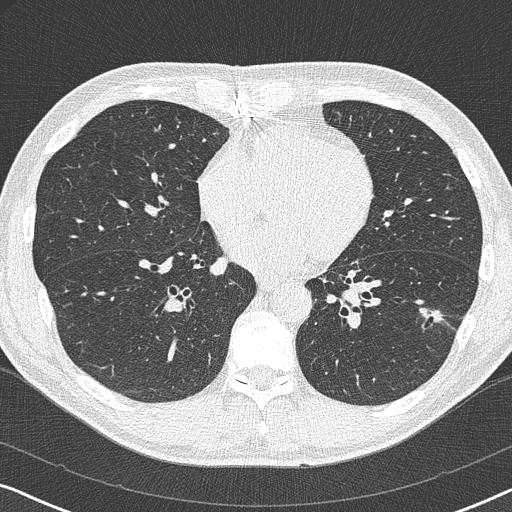
Axial slice from a low-dose chest CT screening exam. First (baseline) screen. Lung window (W 1500 / L -600 HU). 1 mm slice thickness. 120 kVp. Slice 202 of 327 in the series. 512 × 512 image matrix, field of view 330 × 330 mm. Male participant, aged 59 years at enrolment. Current smoker at enrolment.
• Expert reader's lesion annotation, bounding box (x1, y1, x2, y2) in pixels: (416, 301, 452, 342).
• The screening reader recorded 2 non-calcified nodules or masses ≥4 mm on this exam (left lower lobe, right middle lobe); which of them this box marks is not recorded.
• Official screen result: positive, change unspecified: nodule(s) >= 4 mm or enlarging nodule(s), mass(es), or other non-specific abnormalities suspicious for lung cancer.
• Lung cancer was diagnosed 821 days after this screen (after the third annual screen): adenocarcinoma, NOS, left lower lobe, poorly differentiated (G3), stage IA (AJCC 6th edition), 20 mm at pathology.